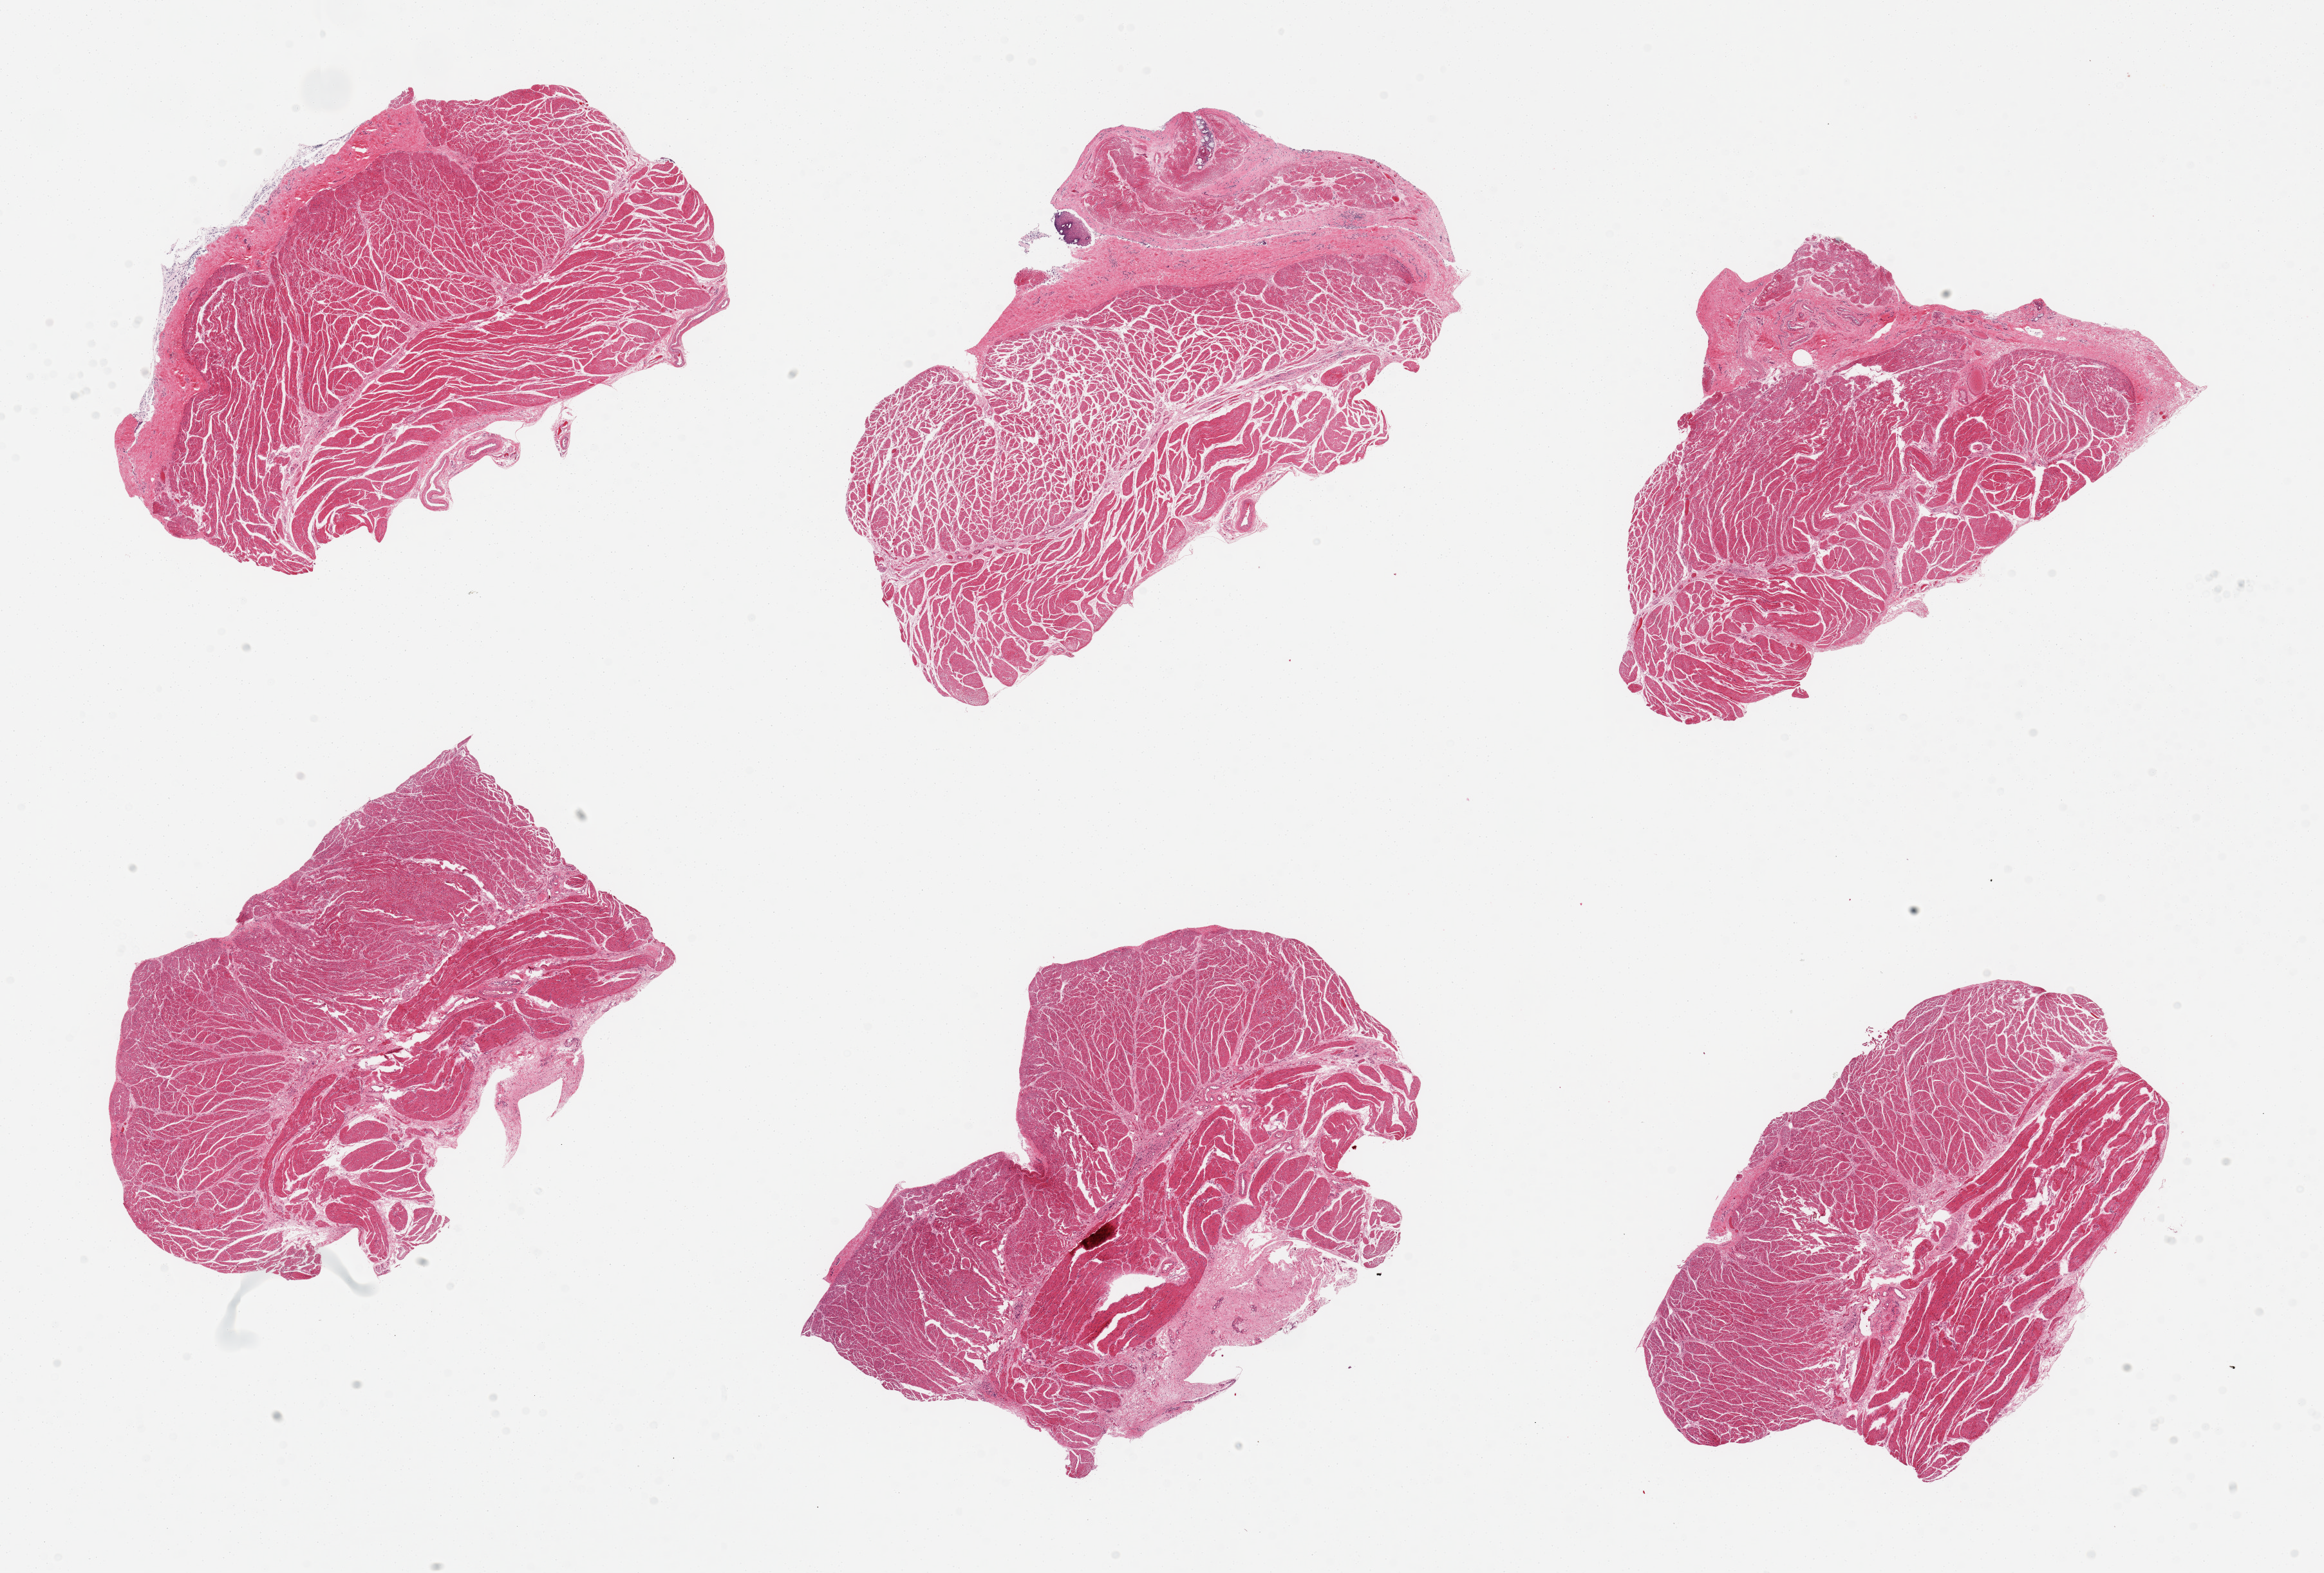
Haematoxylin and eosin whole-slide image, whole scanned area (about 28.5 x 19.3 mm, from a 20x scan) shown as a low-resolution overview, PAXgene-fixed, paraffin-embedded tissue, target tissue: gastroesophageal junction, donor tissue sample. Male donor.
Pathologist's review note for this sample: 6 pieces; well trimmed; 1 small (0.5mm) epithelial fragment.